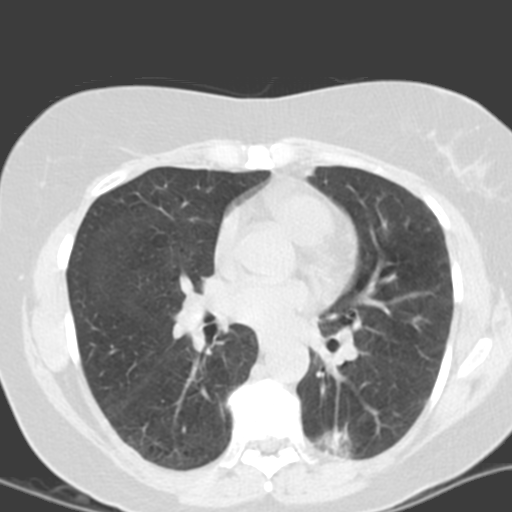
Axial slice from a low-dose chest CT screening exam, second annual screen, lung window (W 1500 / L -600 HU), slice 71 of 161 in the series, 512 × 512 image matrix. Female participant, aged 55 years at enrolment. Current smoker at enrolment.
• Expert reader's lesion annotation, bounding box <305,410,380,468> (left, top, right, bottom; pixels).
• The screening reader recorded 4 non-calcified nodules or masses ≥4 mm on this exam (left lower lobe, left lower lobe, left upper lobe, right middle lobe); which of them this box marks is not recorded.
• Official screen result: positive, other.